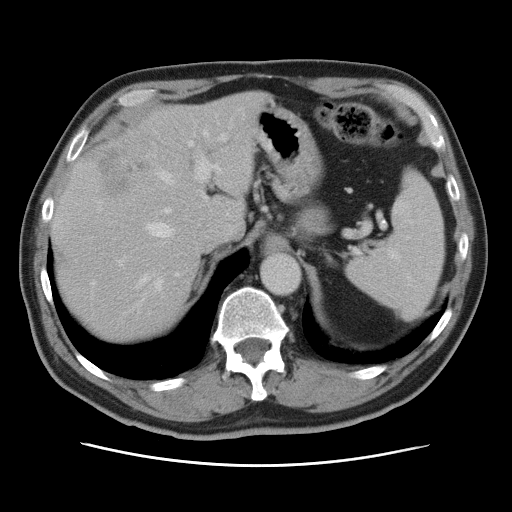
Contrast-enhanced abdominal CT, one axial slice; slice 58 of 80 in the series (ordered by position); 120 kVp; intravenous contrast given; soft-tissue window (W 400 / L 40 HU); 5 mm slice thickness; 512 × 512 image matrix, field of view 370 × 370 mm. Male patient, age 69 years. Case-level facts recorded for this patient, not image findings: diagnosis: colorectal cancer liver metastases, imaged before liver resection; multiple liver metastases: no; largest metastasis: 5 cm; disease in both lobes: yes.
Outlined on this slice (manually delineated by an expert):
- hepatic veins: box from (x=139, y=129) to (x=209, y=291) px
- liver: (x=53, y=92)–(x=263, y=341)
- planned liver remnant (the part of the liver to remain after resection): (x=52, y=92)–(x=263, y=342)
- portal vein (with intrahepatic branches): (x=116, y=119)–(x=234, y=276)
- liver metastasis: (x=88, y=148)–(x=148, y=195)